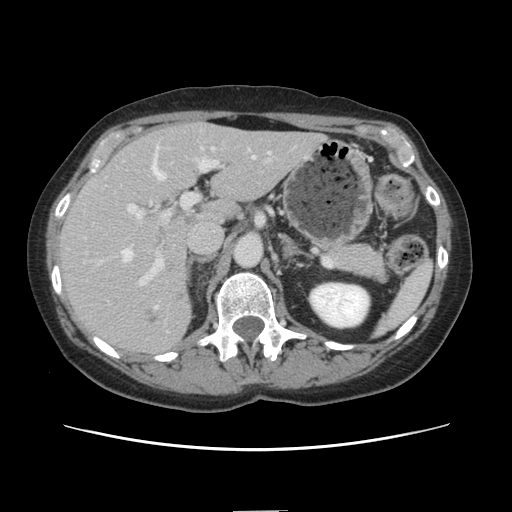
Contrast-enhanced abdominal CT, one axial slice. Position 83 of 141 along the scan axis. 120 kVp. Intravenous contrast given. Soft-tissue window (W 400 / L 40 HU). 2.5 mm slice thickness. 512 × 512 image matrix, field of view 350 × 350 mm. Female patient, age 63 years. Case-level facts recorded for this patient, not image findings: diagnosis: colorectal cancer liver metastases, imaged before liver resection; multiple liver metastases: yes; largest metastasis: 3.2 cm; disease in both lobes: yes.
Annotated regions visible in this slice (manually delineated by an expert):
- hepatic veins: box from (x=99, y=144) to (x=255, y=308) px
- liver: (x=59, y=123)–(x=321, y=354)
- planned liver remnant (the part of the liver to remain after resection): (x=176, y=124)–(x=321, y=222)
- portal vein (with intrahepatic branches): (x=127, y=149)–(x=222, y=287)
- liver metastasis: (x=165, y=262)–(x=177, y=273)
- liver metastasis: (x=175, y=292)–(x=185, y=301)
- liver metastasis: (x=143, y=309)–(x=159, y=325)